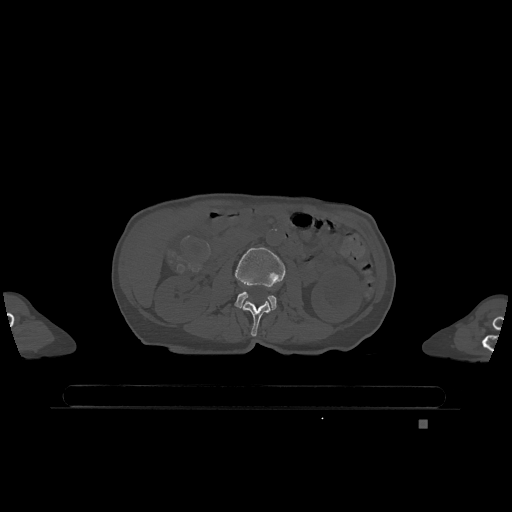
CT including the spine, one axial slice; position 387 of 1317 along the scan axis; bone window (W 1800 / L 400 HU); 0.5 mm slice thickness; 512 × 512 image matrix. Patient: female, 74 years. Case-level facts recorded for this patient, not image findings: primary cancer: lung.
Structures marked on this image (semi-automatic segmentation, software-assisted and operator-edited):
- L2 vertebra: box from (x=243, y=301) to (x=271, y=337) px
- L3 vertebra: (x=235, y=247)–(x=285, y=310)